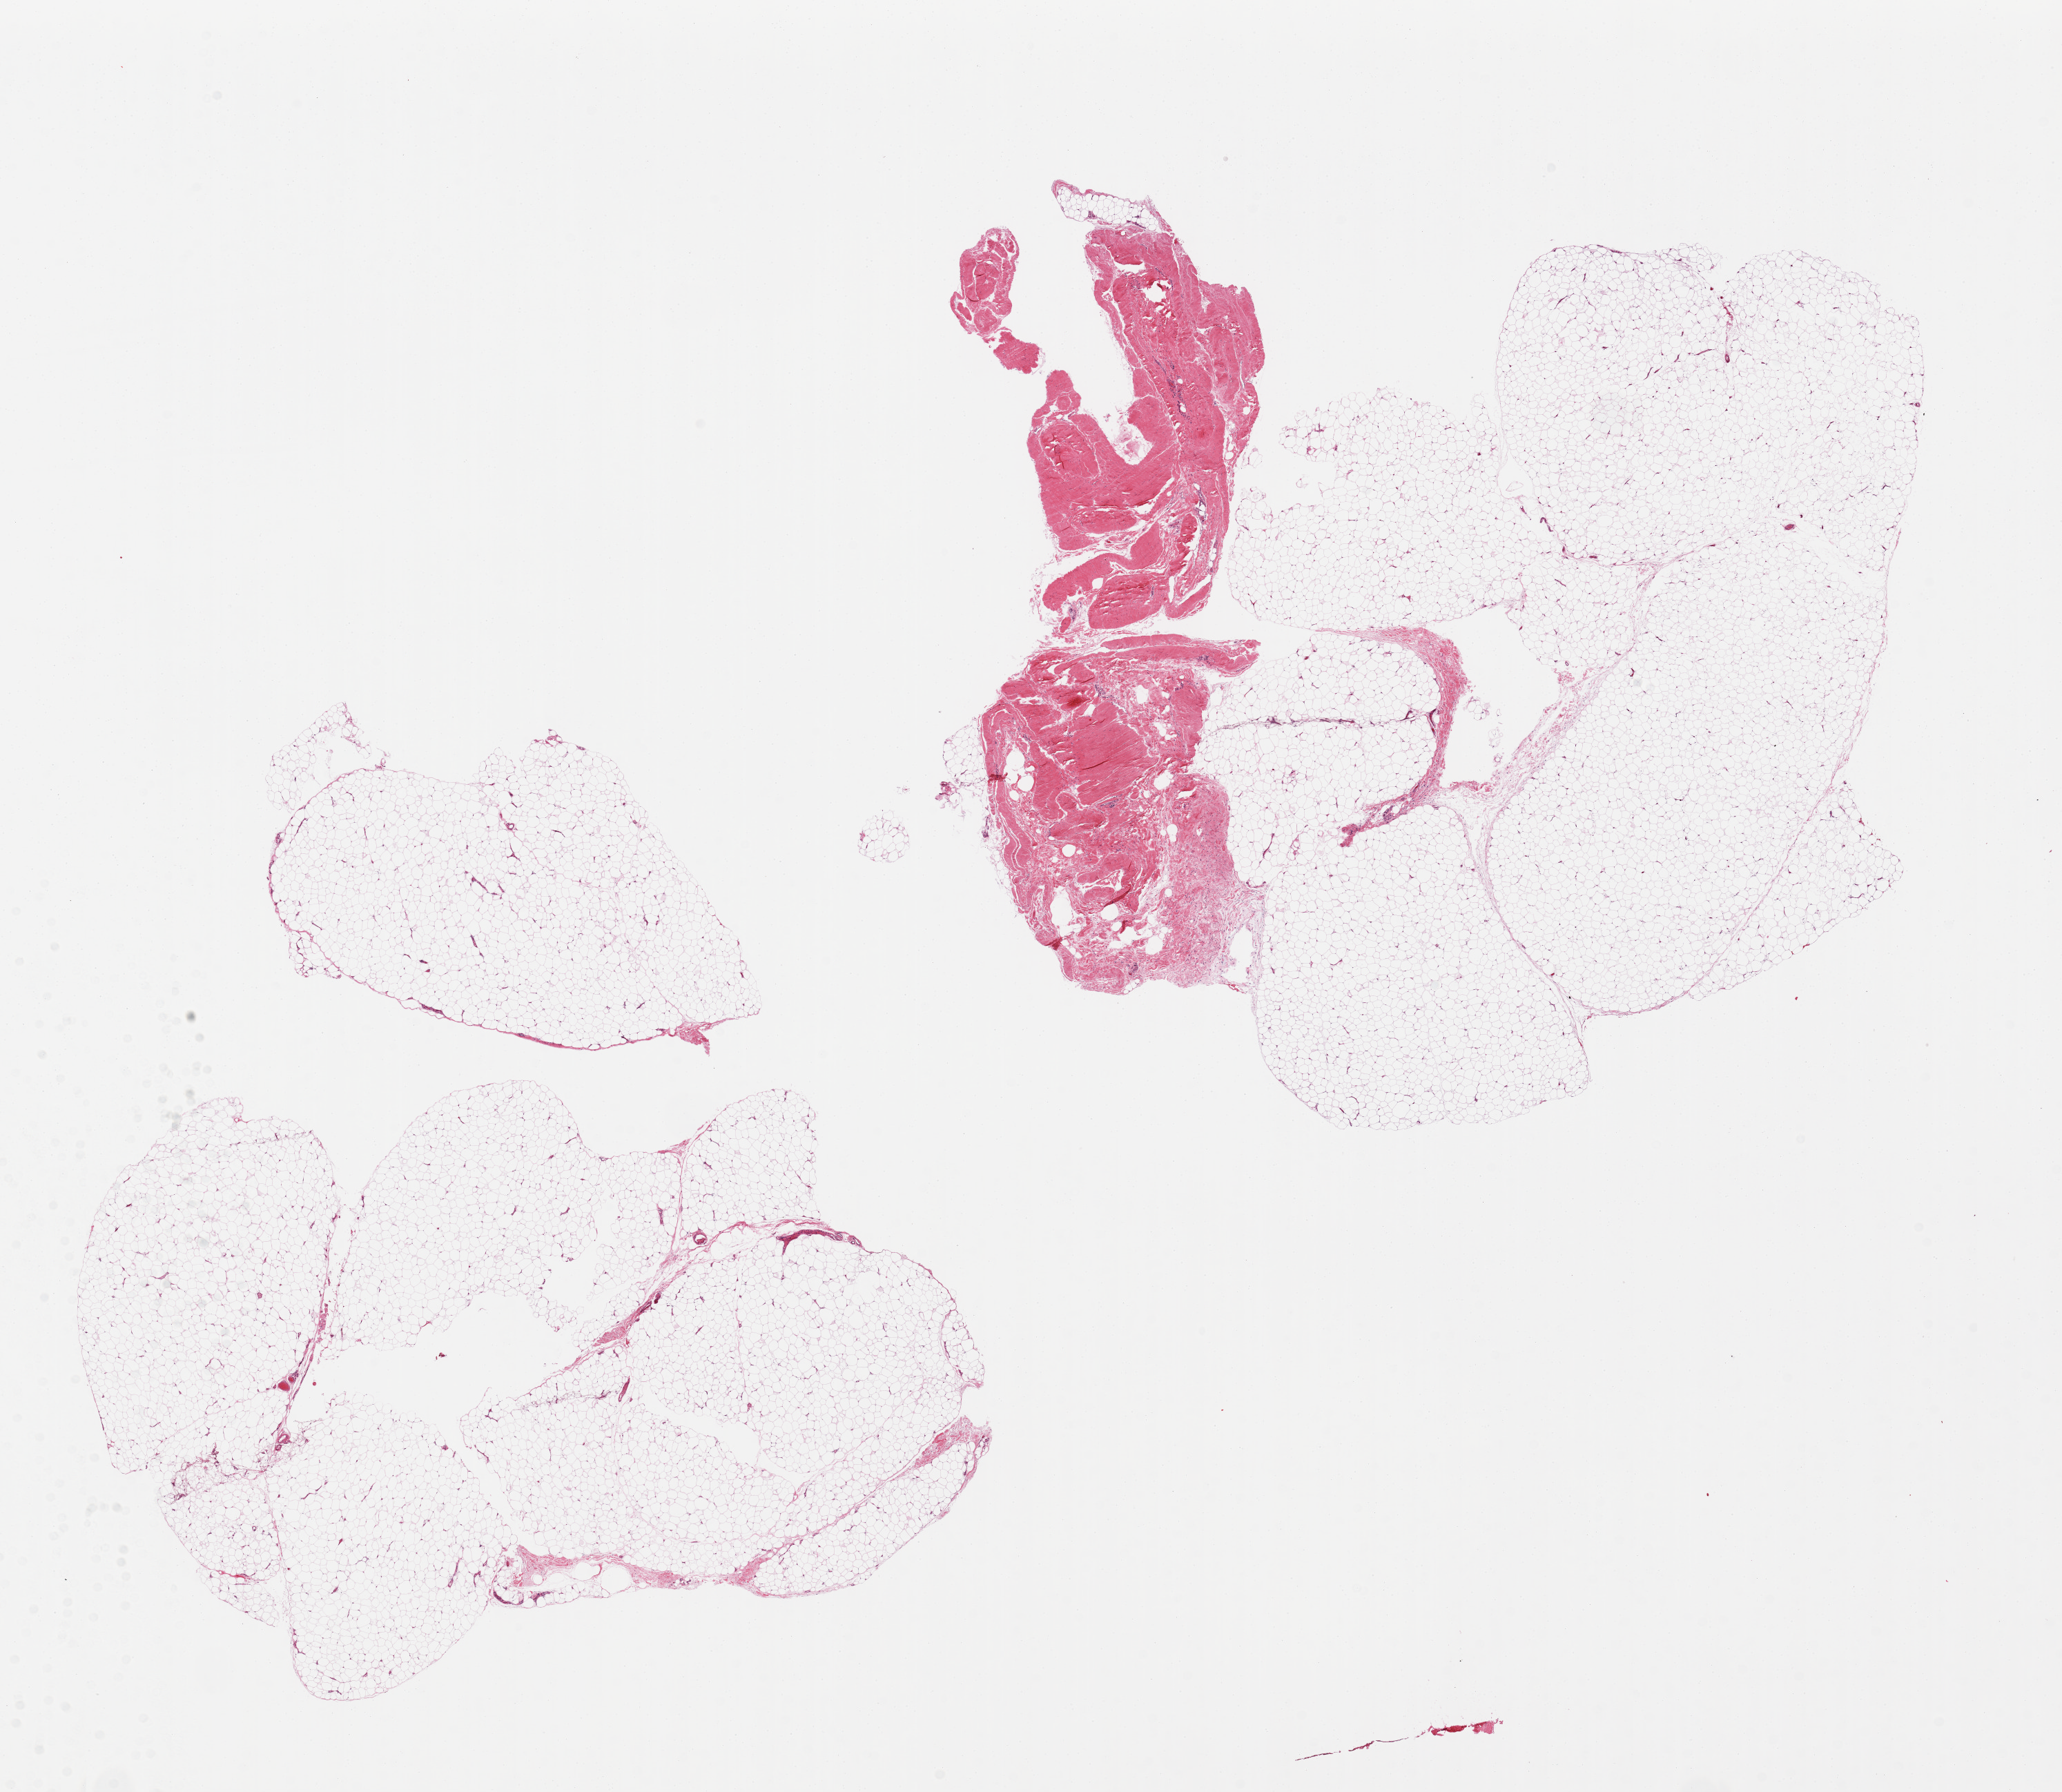
Whole-slide image, haematoxylin and eosin stain — shown as a low-resolution overview of the whole scanned area (about 23.6 x 20.5 mm). PAXgene-fixed, paraffin-embedded tissue. Sampled site (target tissue): adipose tissue. Tissue donor sample. Male donor.
Reviewer comment on this tissue sample: 2 pieces, one piece is ~20% tendon/fibrous tissue.